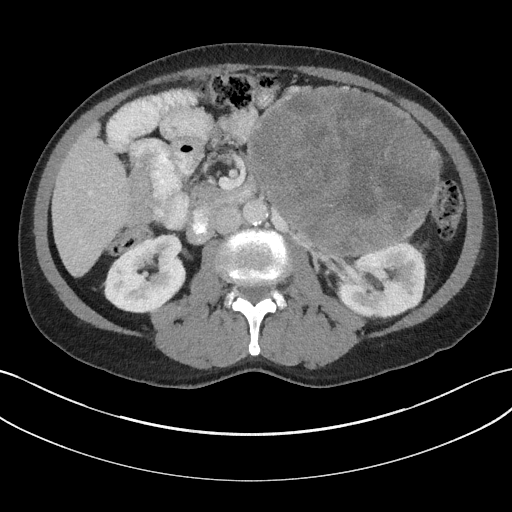
Contrast-enhanced abdominal CT, one axial slice. Slice 90 of 147 in the series (ordered by position). 100 kVp. Soft-tissue window (W 400 / L 40 HU). 512 × 512 image matrix, field of view 384 × 384 mm. Patient: male, 58 years. Case-level facts recorded for this patient, not image findings: diagnosis: adrenocortical carcinoma; tumour side: left adrenal; tumour size at pathology: 22 cm; Ki-67 index: 26 %; stage (as recorded): 2.
Outlined on this slice (semi-automatic segmentation, software-assisted and operator-edited):
- mass: box from (x=249, y=87) to (x=438, y=254) px